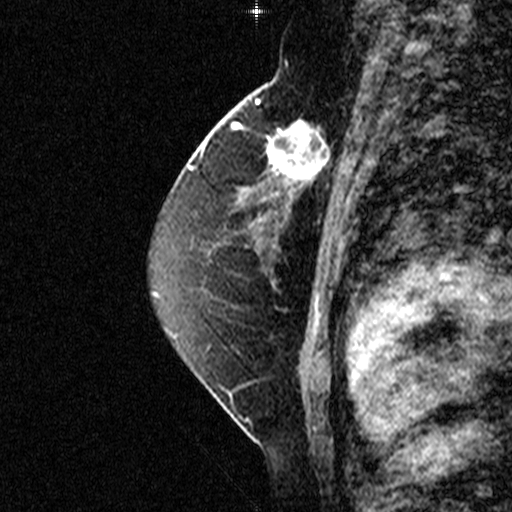
Breast MRI (dynamic contrast-enhanced), one sagittal slice. Position 25 of 44 along the scan axis. Dynamic contrast-enhanced study with each time point stored as its own series, time point 2 of 3 at this slice position (early post-contrast, ordered by acquisition time). 1.5 T. TE 4.5 ms, TR 11 ms. 3 mm slice thickness. 512 × 512 image matrix, field of view 200 × 200 mm. Patient: female, 49 years. From the clinical record (not read from this slice): setting: breast cancer imaged before/during neoadjuvant chemotherapy; receptor status: triple-negative.
Structures marked on this image (semi-automatically segmented with operator editing):
- analysis volume of interest (the breast-tissue region the enhancement analysis was run in; not a lesion): bounding box [x1, y1, x2, y2] px = [254, 112, 347, 207]
- tumour enhancement mask (voxels above the 90 % enhancement threshold inside the analysis volume of interest): [258, 118, 347, 207]